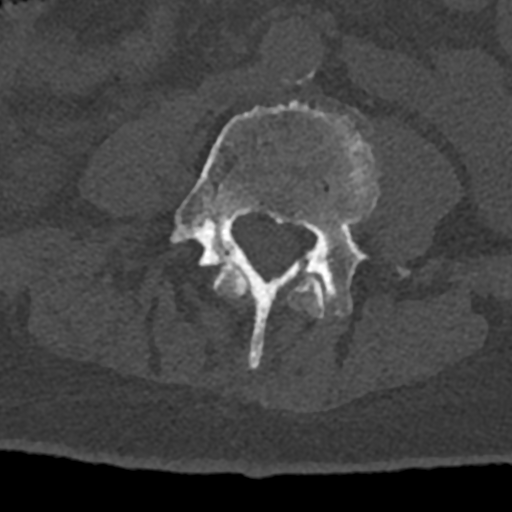
CT including the spine, one axial slice. Slice 269 of 797 in the series (ordered by position). Reconstruction kernel Br40s/3. Bone window (W 1800 / L 400 HU). 0.5 mm slice thickness. 512 × 512 image matrix. Patient: male, 74 years. From the clinical record (not read from this slice): primary cancer: renal.
Structures marked on this image (semi-automatic segmentation, software-assisted and operator-edited):
- L3 vertebra: bounding box [x1, y1, x2, y2] px = [212, 264, 329, 319]
- L4 vertebra: [170, 80, 409, 368]